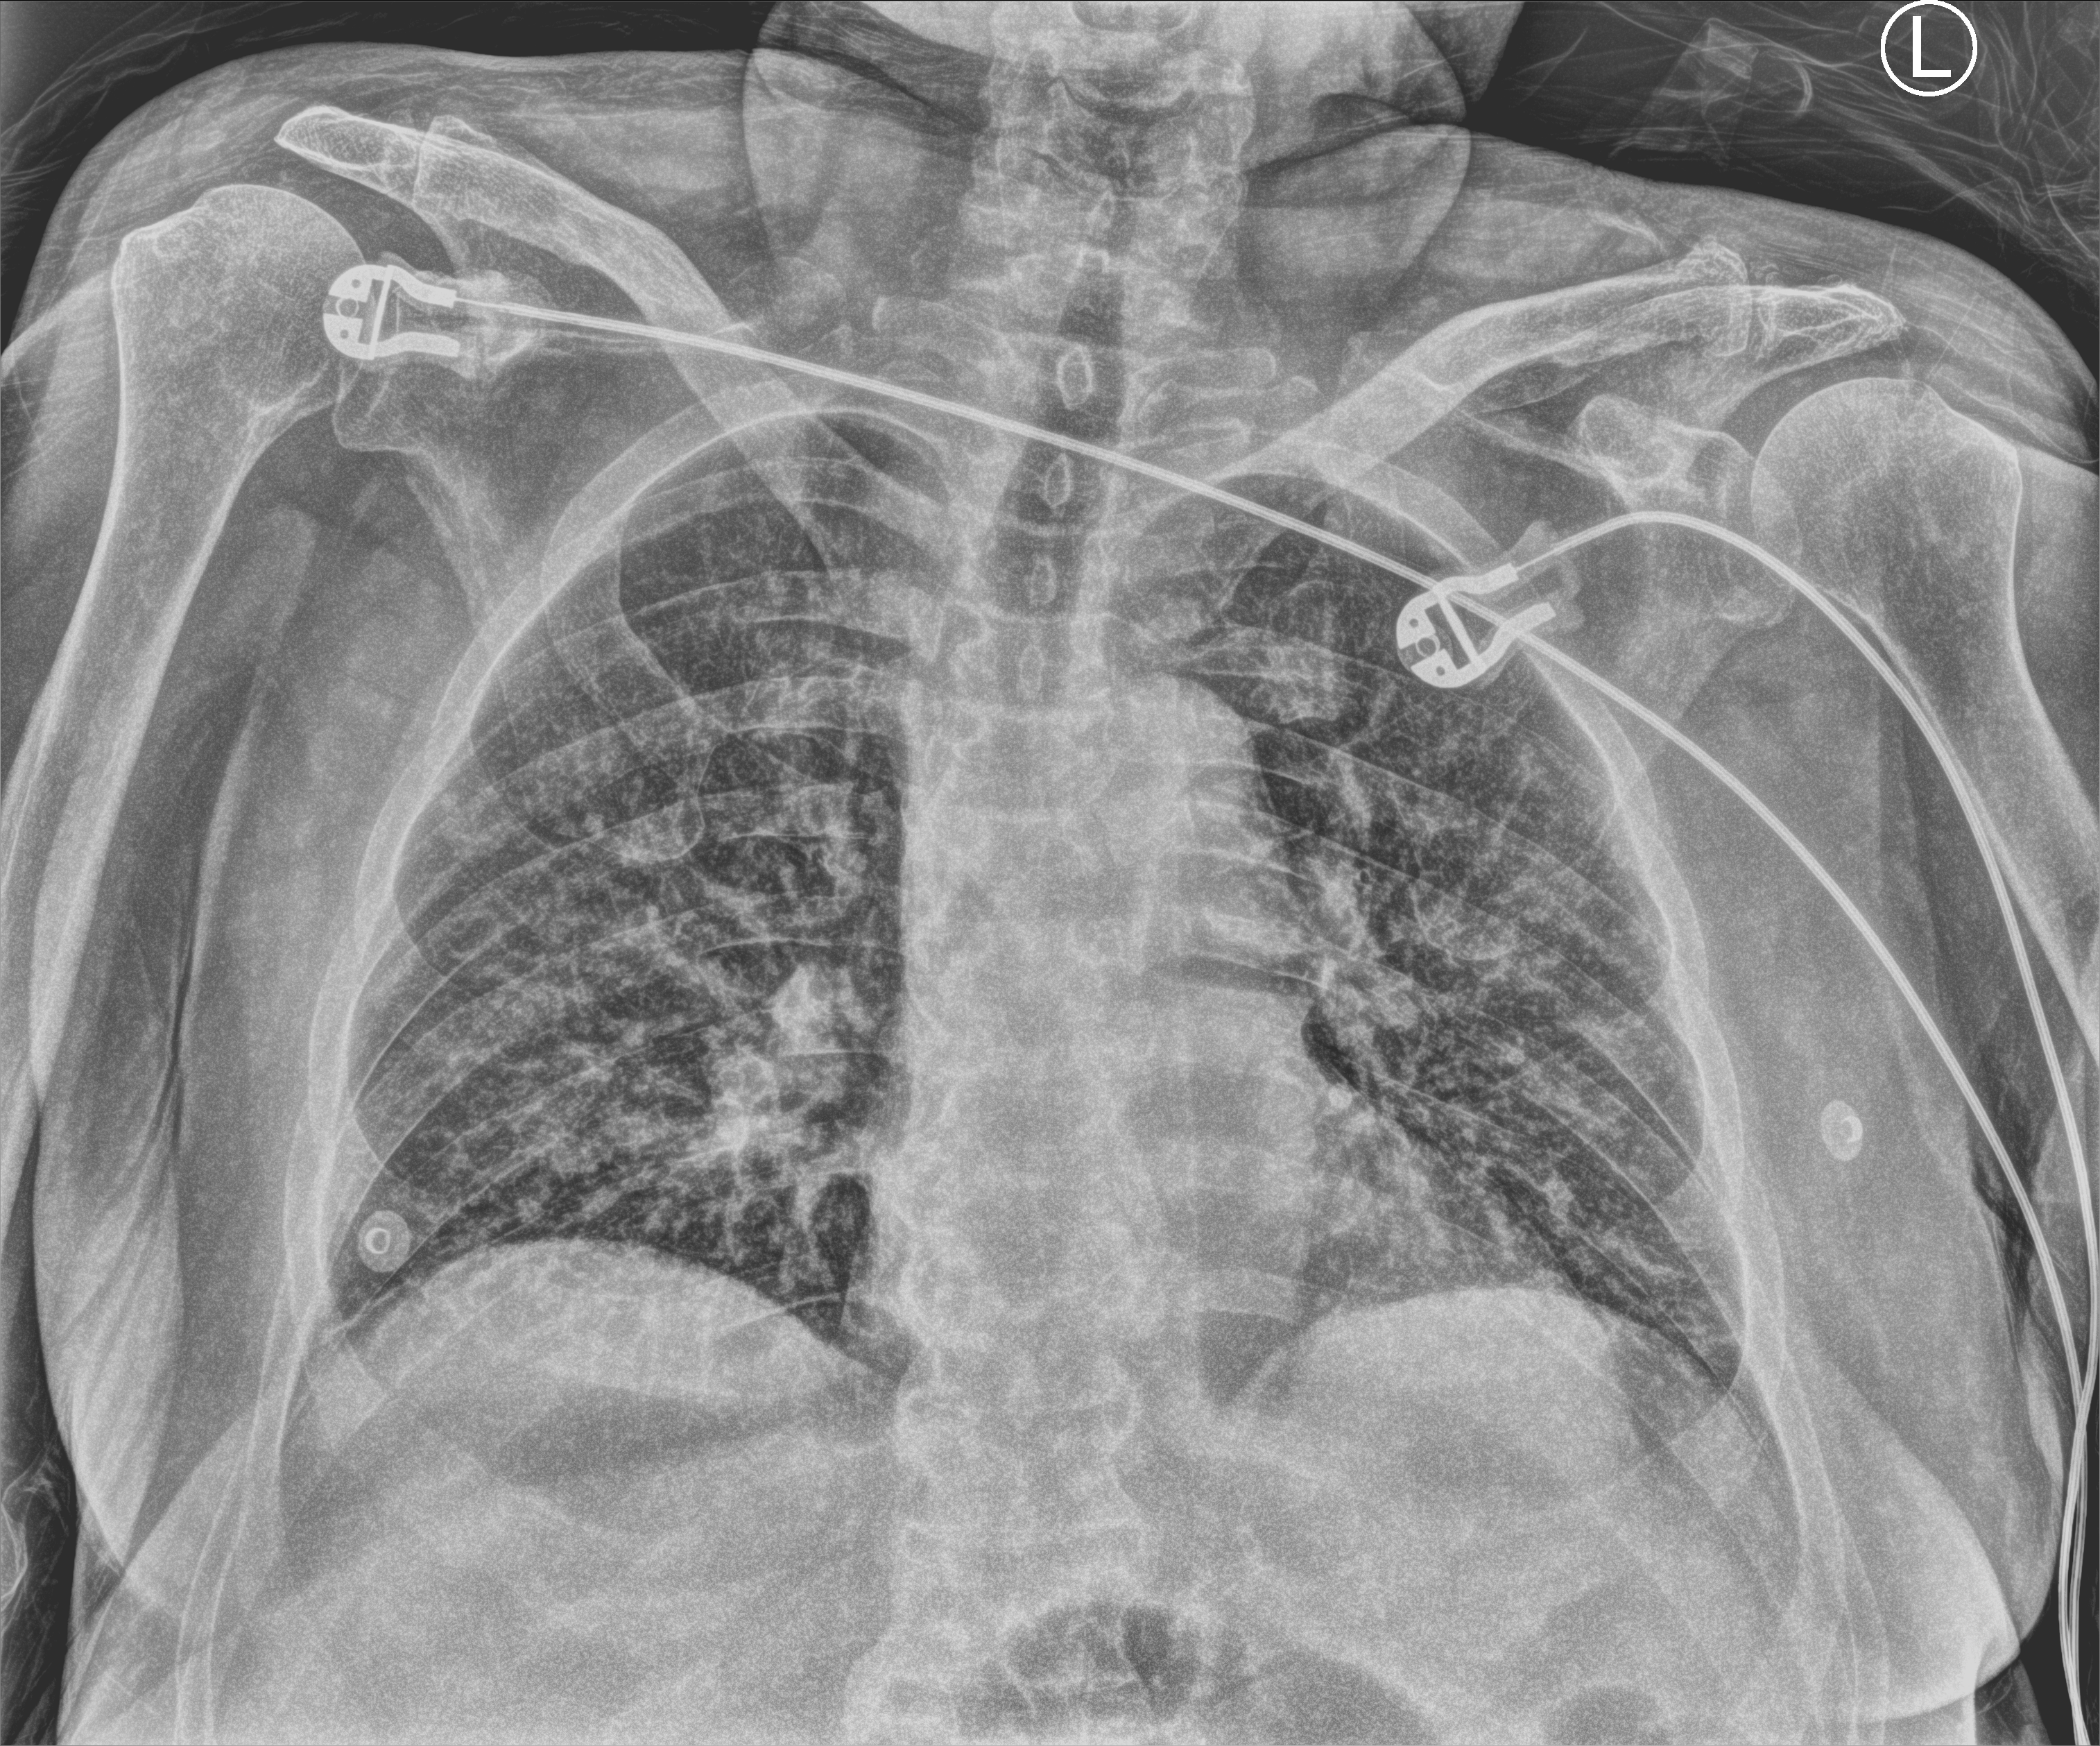
Portable chest radiograph; anteroposterior (AP) projection. Male patient hospitalised with COVID-19, age 60–74 years.
Hospital-stay facts (about this admission, not read from this image; timing relative to this image not recorded): mechanically ventilated during this hospital stay: no; admitted to intensive care during this hospital stay: no.